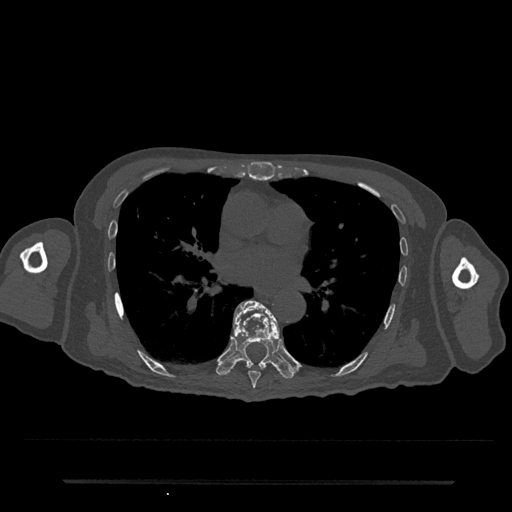
CT including the spine, one axial slice; slice 448 of 797 in the series (ordered by position); reconstruction kernel Br40s/3; 120 kVp; bone window (W 1800 / L 400 HU); 0.5 mm slice thickness; 512 × 512 image matrix, field of view 427 × 427 mm. Patient: male, 74 years. Case-level facts recorded for this patient, not image findings: primary cancer: prostate.
Outlined on this slice (semi-automatically segmented with operator editing):
- T7 vertebra: bounding box <233,302,280,389> (left, top, right, bottom; pixels)
- T8 vertebra: <216,300,295,379>